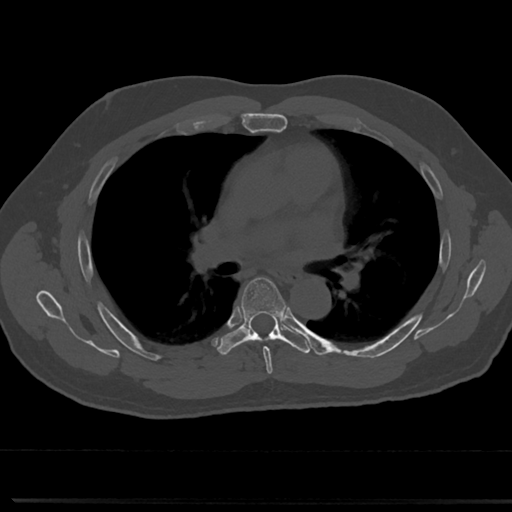
CT including the spine, one axial slice. Position 466 of 817 along the scan axis. Reconstruction kernel Br40s/3. Bone window (W 1800 / L 400 HU). 512 × 512 image matrix, field of view 355 × 355 mm. Male patient, age 61 years. From the clinical record (not read from this slice): primary cancer: prostate.
Outlined on this slice (semi-automatic segmentation, software-assisted and operator-edited):
- T5 vertebra: bounding box (x1, y1, x2, y2) in pixels: (243, 279, 283, 364)
- T6 vertebra: (218, 275, 306, 354)